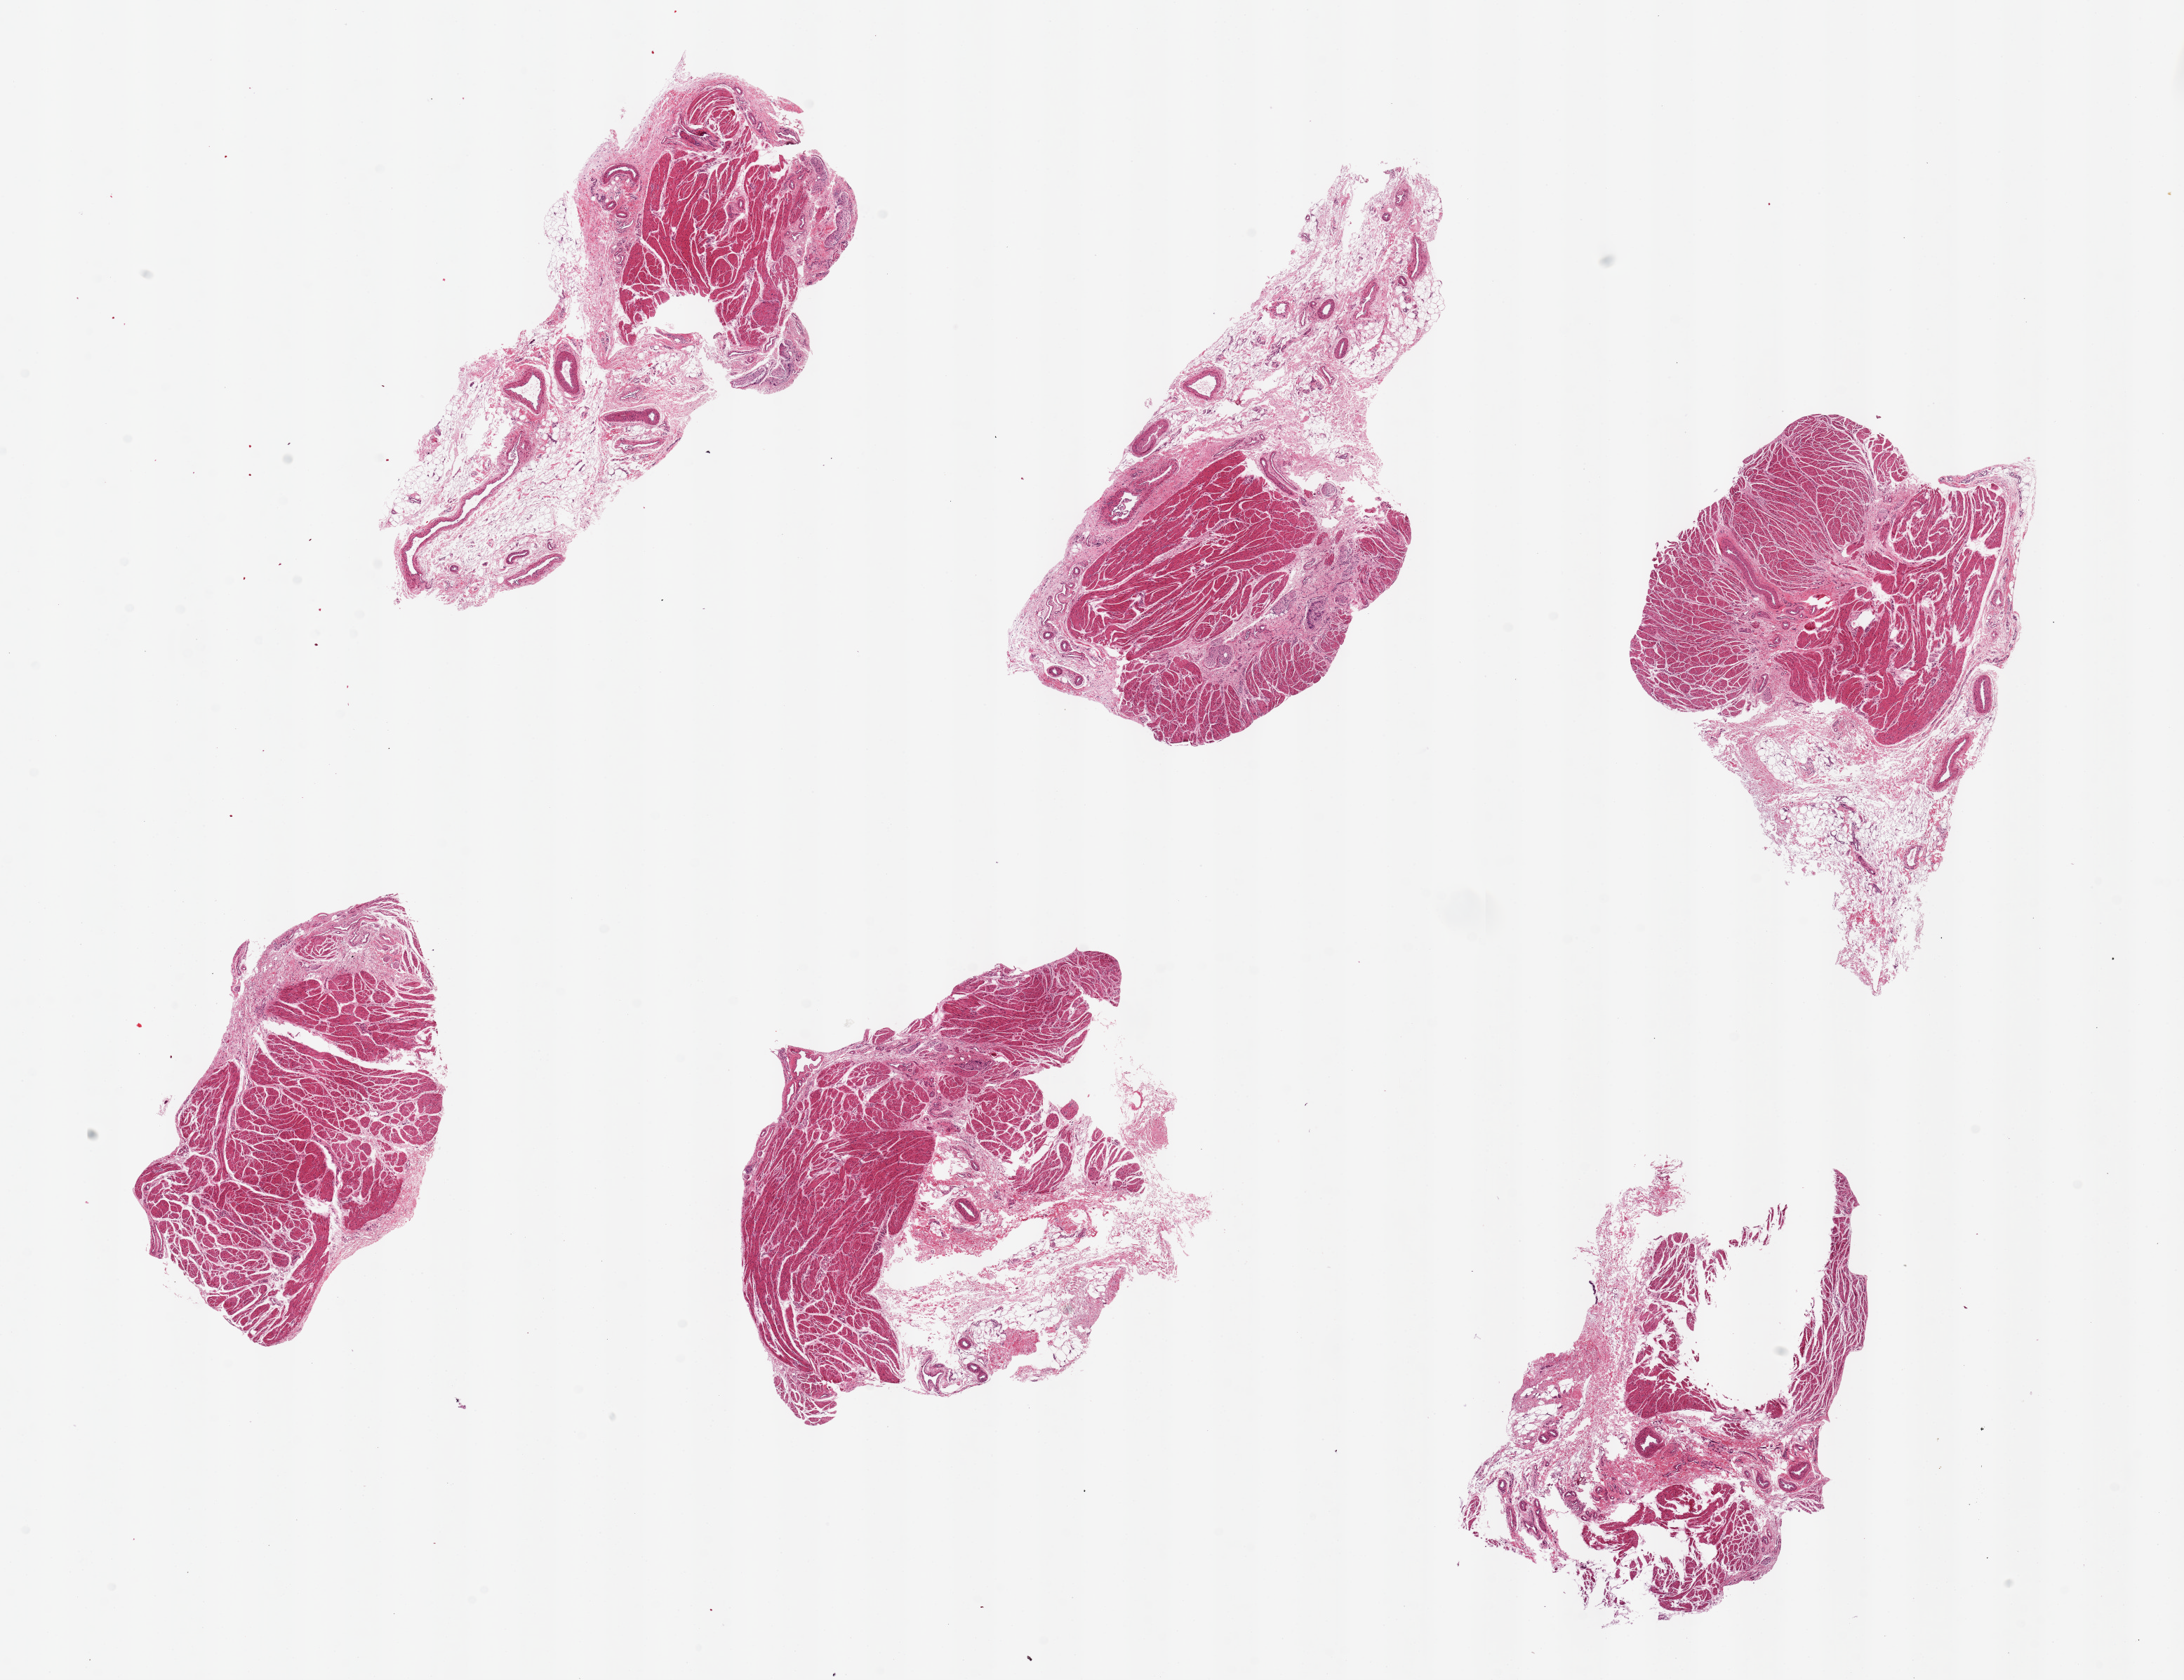
Haematoxylin and eosin whole-slide image — shown as a low-resolution overview of the whole scanned area (about 24.6 x 18.9 mm); PAXgene-fixed, paraffin-embedded tissue; target tissue: gastroesophageal junction; tissue donor sample. Donor: male.
Review note (as recorded): 6 pieces ~7x3mm, 60% muscularis overall, adherent fibroadipose nubbins.